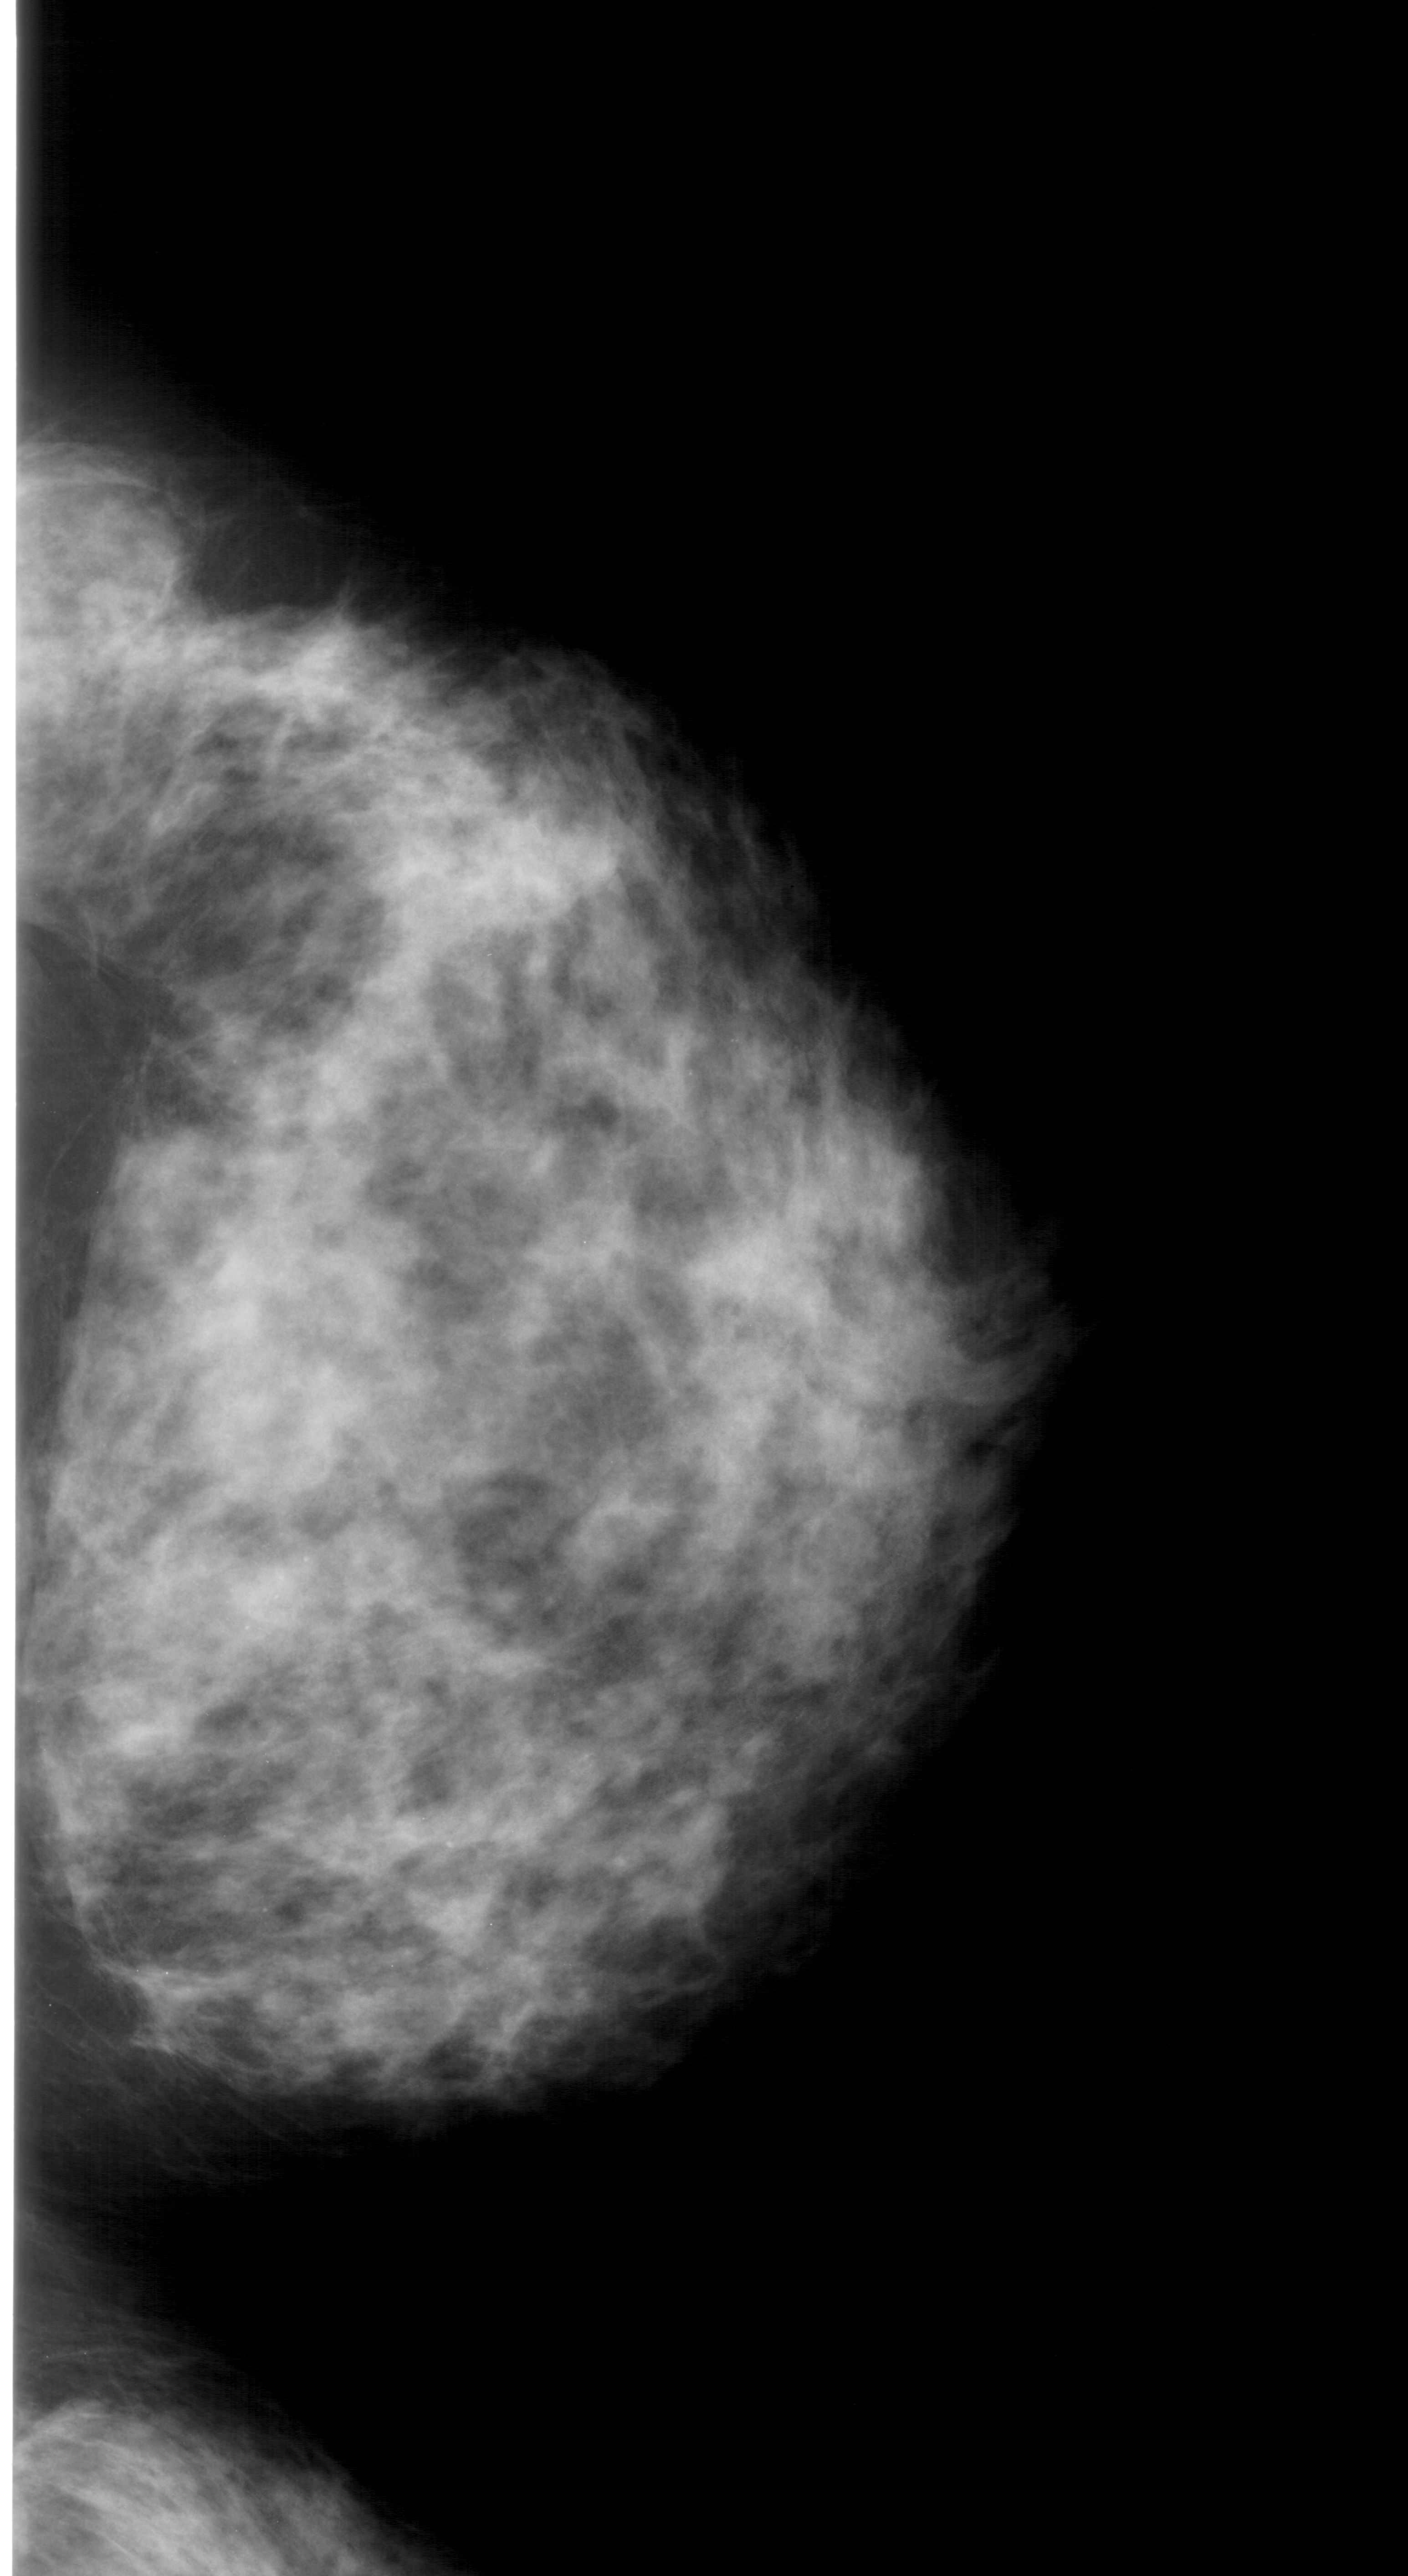
Digitized screen-film mammogram, right breast, craniocaudal (CC) view, BI-RADS breast density category 3 (scale 1–4).
Marked findings (only marked abnormalities are described; nothing is implied about the rest of the image): calcifications, morphology pleomorphic, distribution clustered; BI-RADS assessment category 4; subtlety rating 2 on a 1 (subtle) to 5 (obvious) scale; pathology result (as recorded, not read from the image): benign.